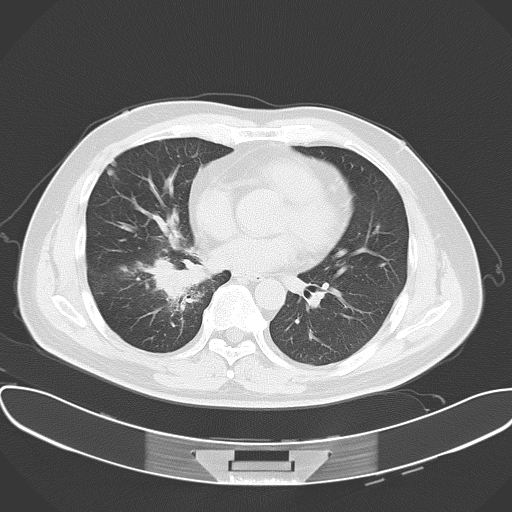
Chest CT, one axial slice. Position 26 of 57 along the scan axis. 120 kVp. Lung window (W 1500 / L -600 HU). 5 mm slice thickness. 512 × 512 image matrix, field of view 388 × 388 mm. Patient: male, 48 years. From the clinical record (not read from this slice): clinical TNM (as recorded): T1a N1 M1c; histopathological grade: G3.
Outlined on this slice (bounding box drawn by a radiologist):
- lung tumour (recorded histology: adenocarcinoma): bounding box (x1, y1, x2, y2) in pixels: (156, 256, 206, 305)